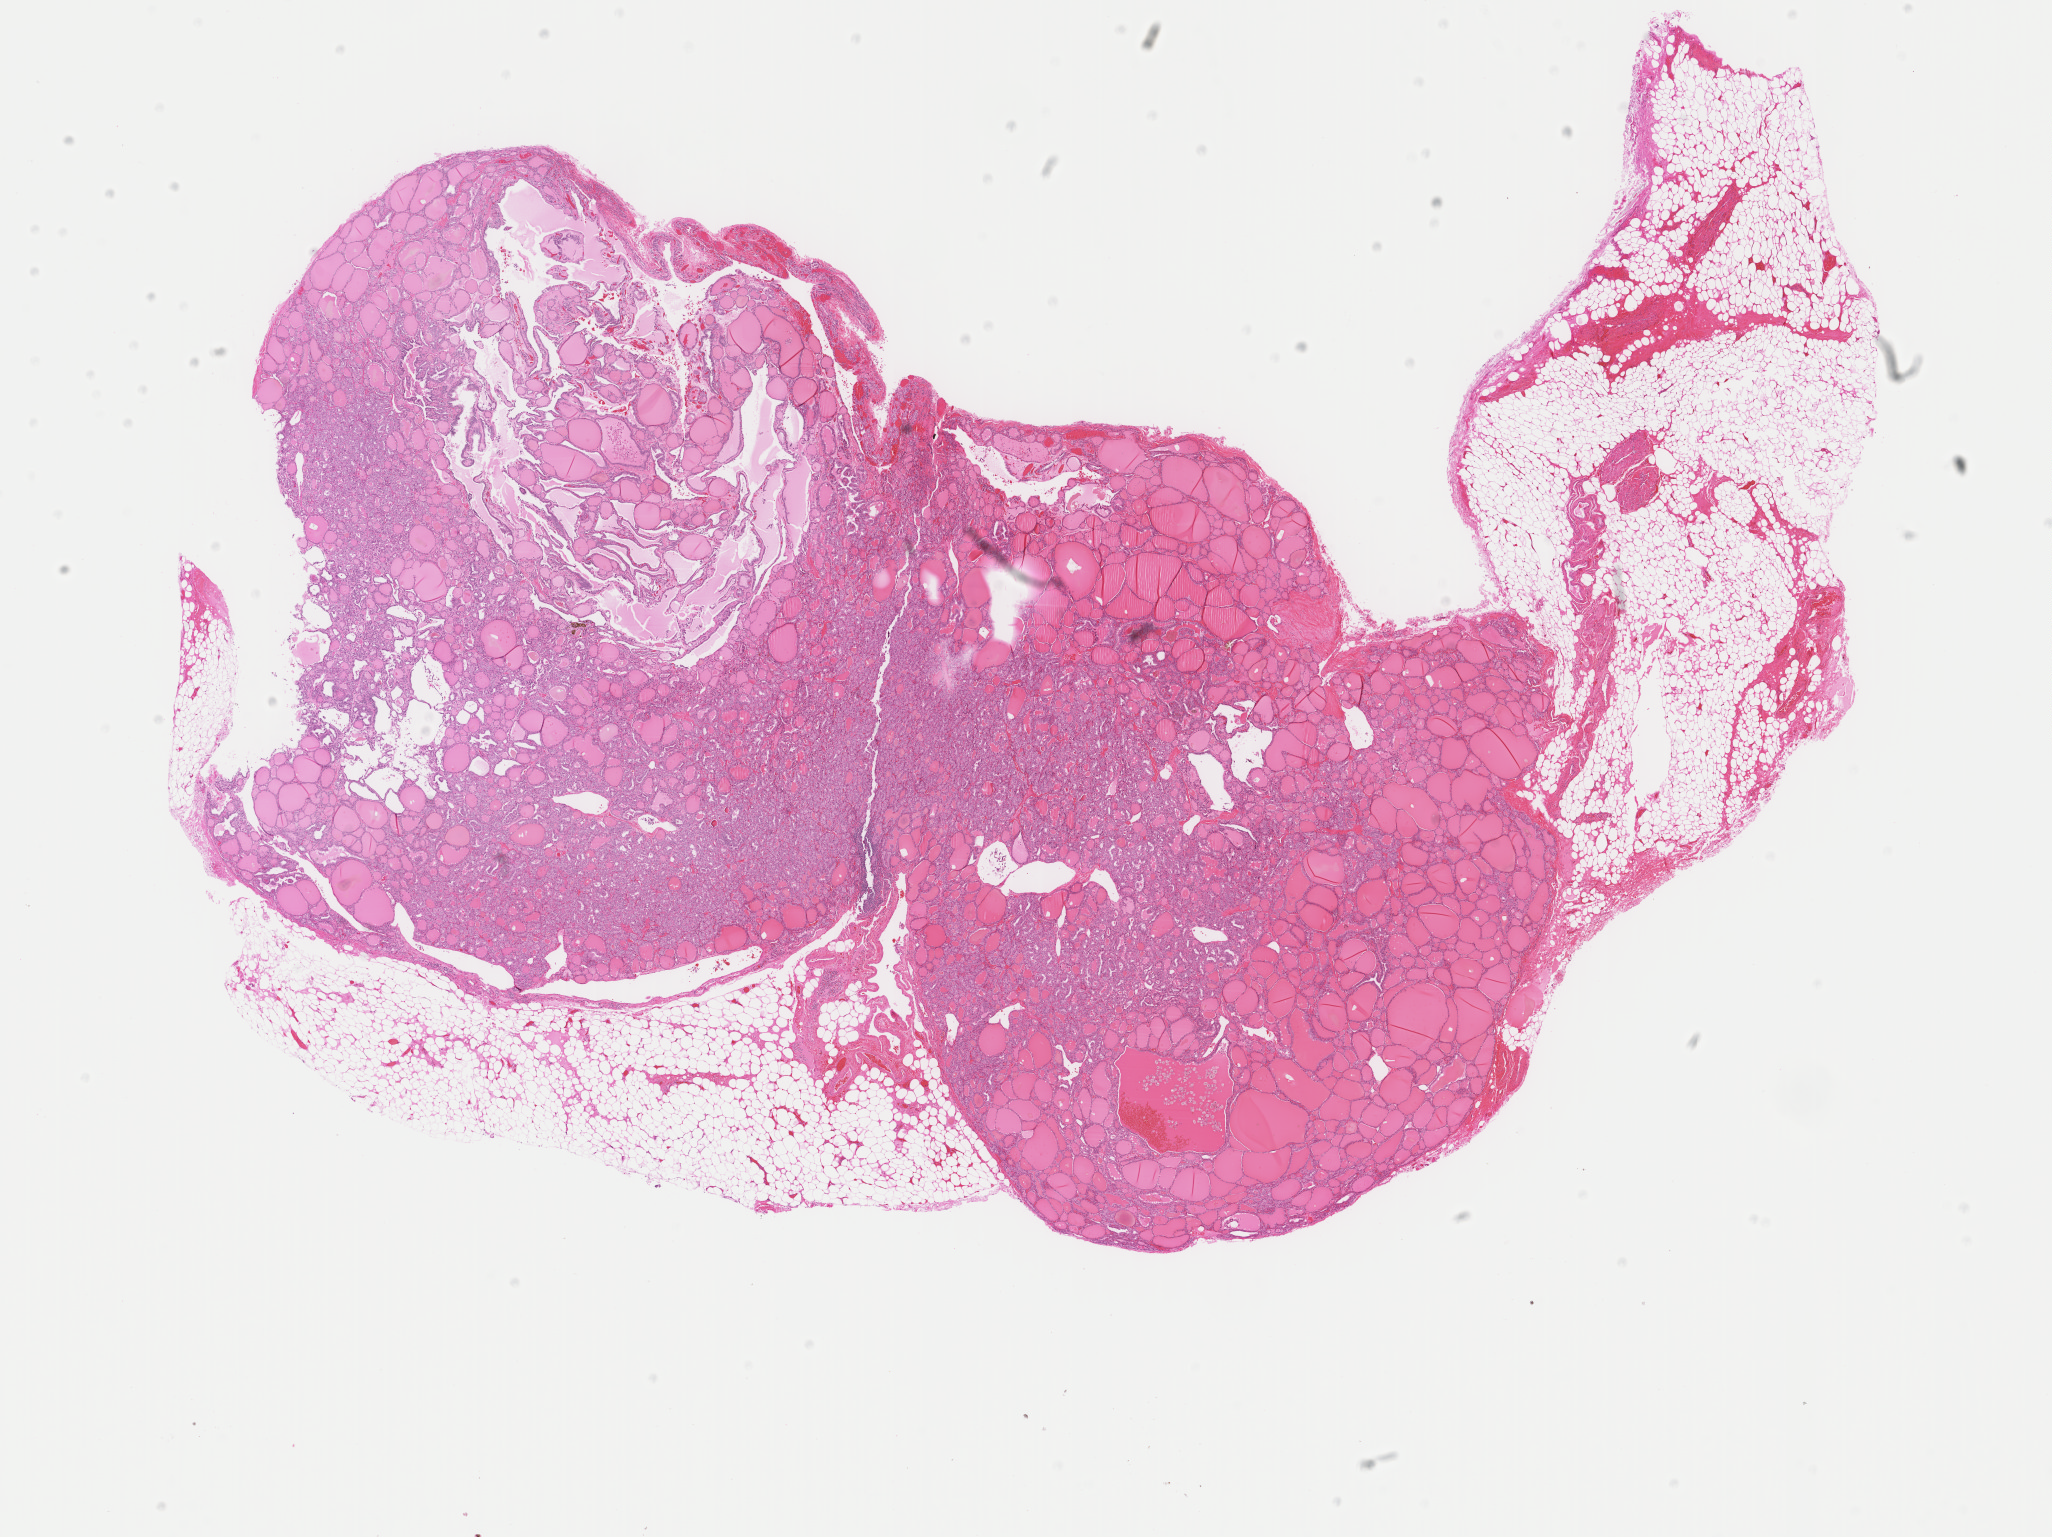
Whole-slide histology image, H&E-stained — whole scanned area (about 16.3 x 12.2 mm, acquisition: 40x scan) shown as a low-resolution overview, formalin-fixed paraffin-embedded (FFPE) diagnostic section, primary tumour sample from the thyroid. Male patient; age at initial diagnosis 58 years.
Histologic diagnosis: Papillary adenocarcinoma, NOS (thyroid gland). TNM: T2 N0 MX. AJCC pathologic stage: II. Laterality: right.